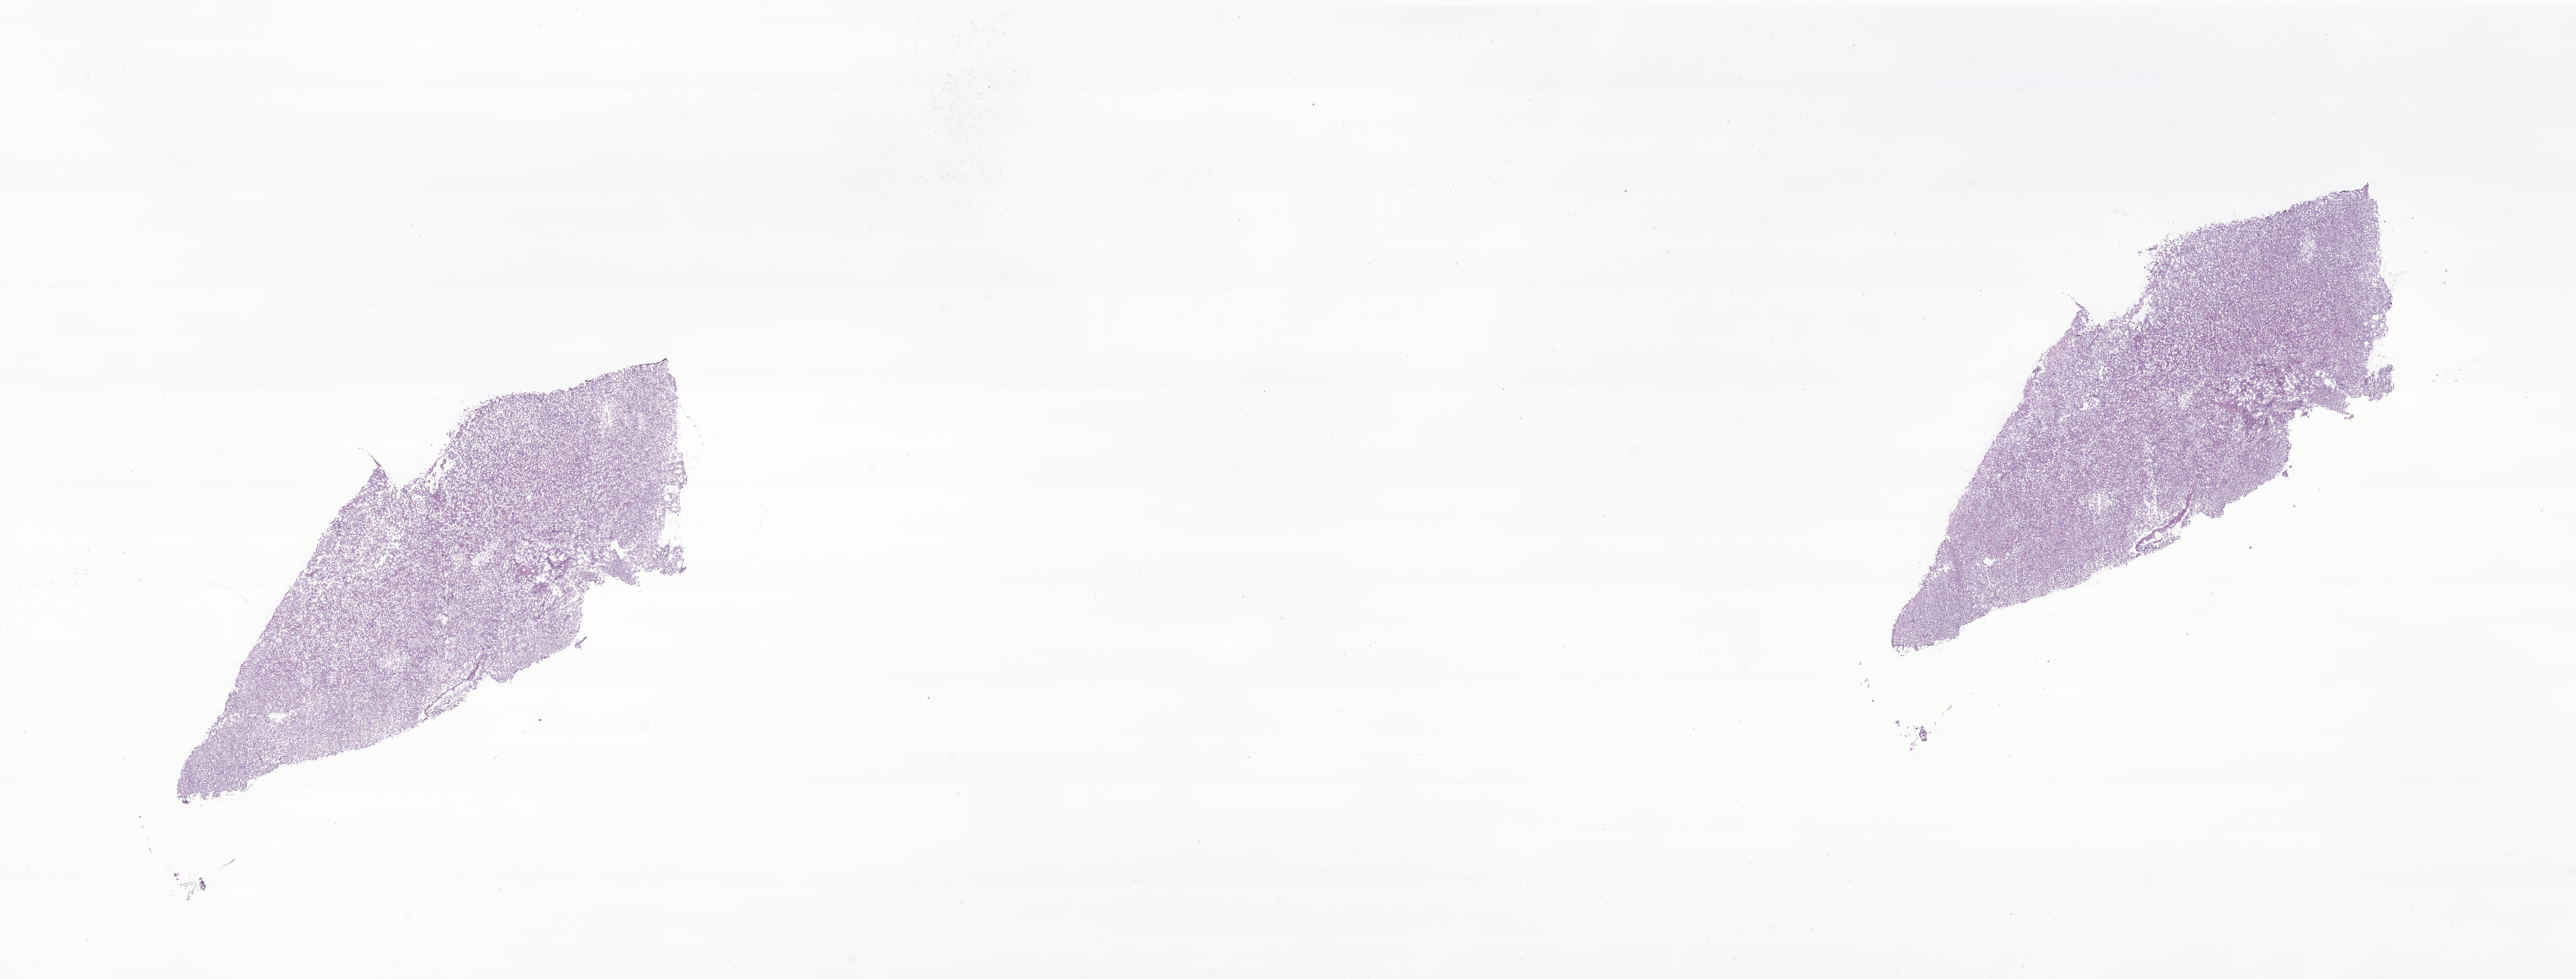
Digitized hematoxylin and eosin (H&E)-stained section of tumor tissue from the brain, low-resolution overview of the scanned area, about 27.7 x 10.5 mm, frozen section. Patient male; age 124 months (10 years 4 months).
Recorded diagnosis: Glioma, malignant.